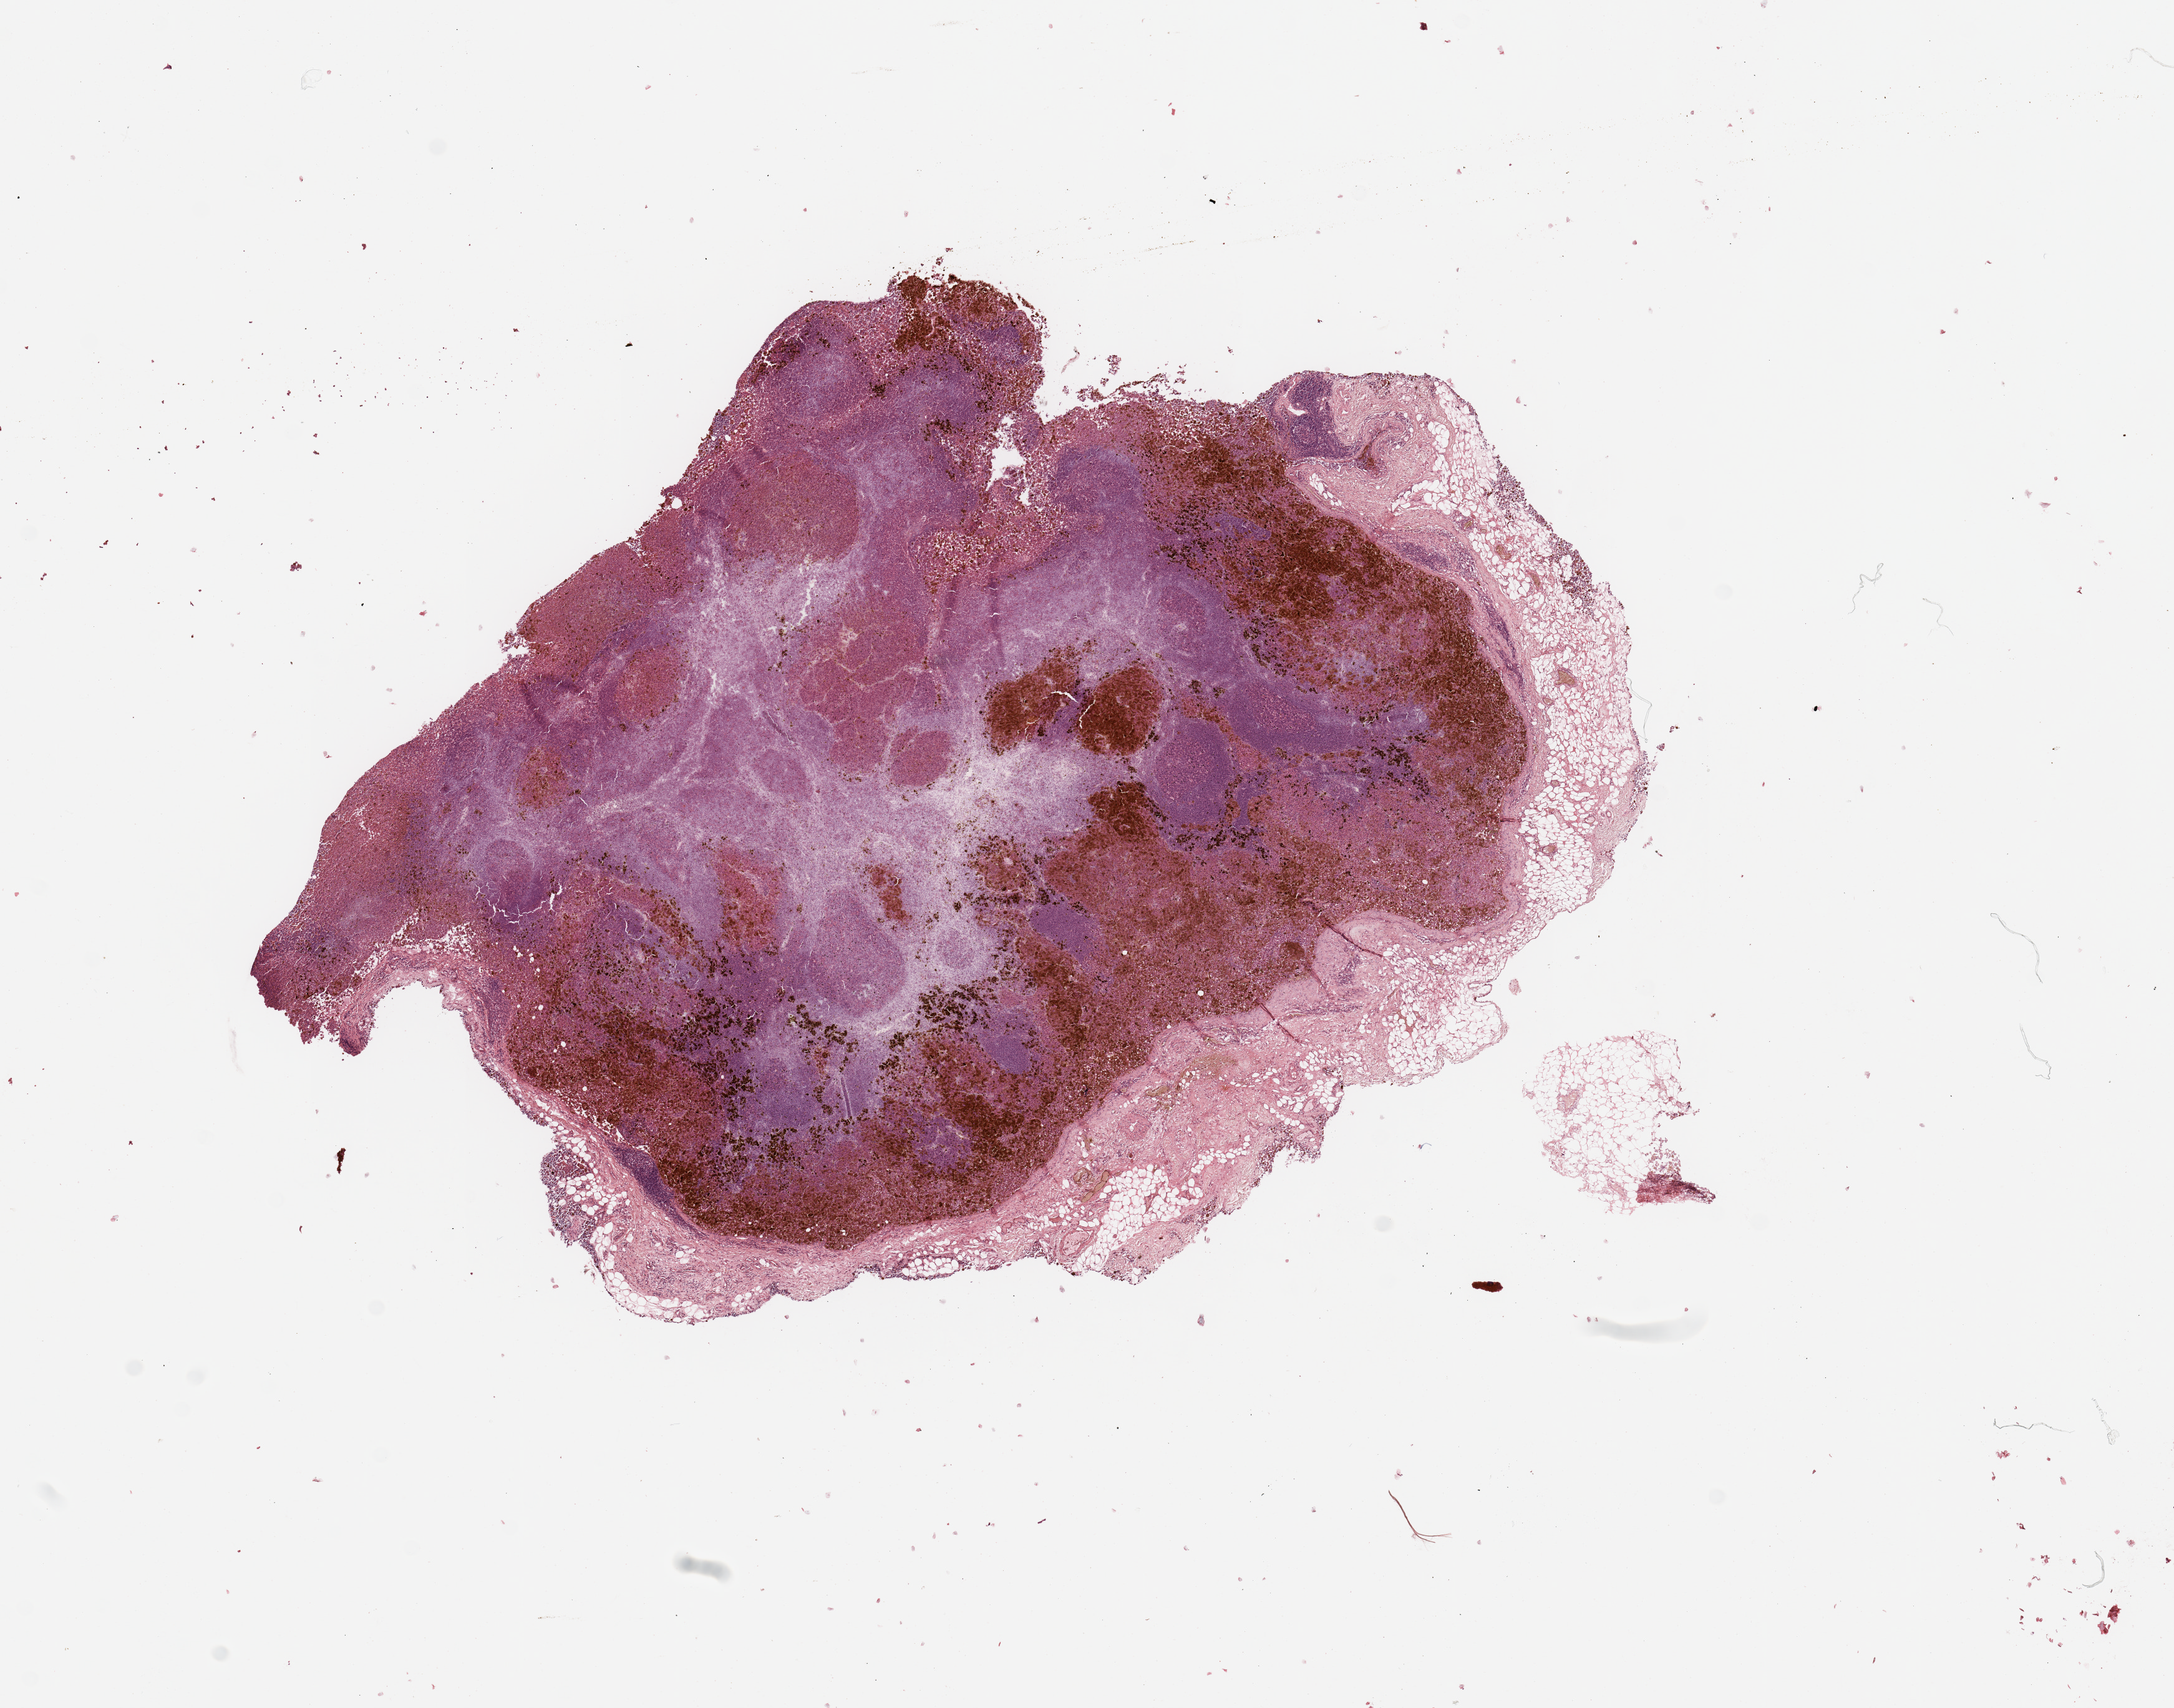
H&E whole-slide image, low-resolution overview of the scanned area, about 13.8 x 10.8 mm; melanoma tumour tissue; sampled site not recorded. Female, 44 y/o.
Primary tumour site (as recorded): trunk. Patient diagnosis (cohort enrolment): cutaneous melanoma (skin).